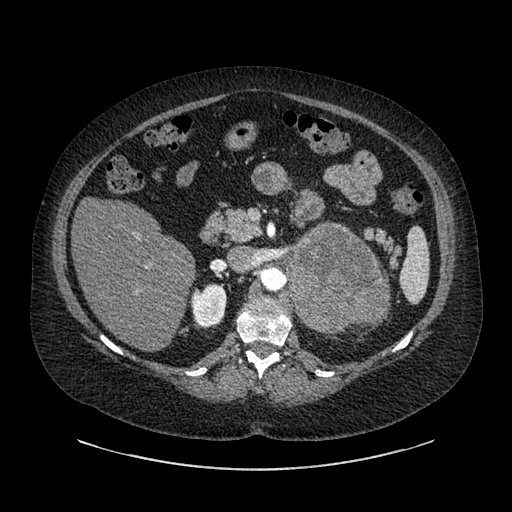
Contrast-enhanced abdominal CT, one axial slice. Slice 547 of 769 in the series (ordered by position). Reconstruction kernel SOFT. 120 kVp. Intravenous contrast given. Soft-tissue window (W 400 / L 40 HU). 0.62 mm slice thickness. 512 × 512 image matrix. Female patient, age 61 years. Case-level facts recorded for this patient, not image findings: diagnosis: adrenocortical carcinoma; tumour side: left adrenal; tumour size at pathology: 13 cm; Ki-67 index: 79 %; stage (as recorded): 2.
Structures marked on this image (semi-automatically segmented with operator editing):
- mass: bounding box (x1, y1, x2, y2) in pixels: (290, 226, 386, 333)